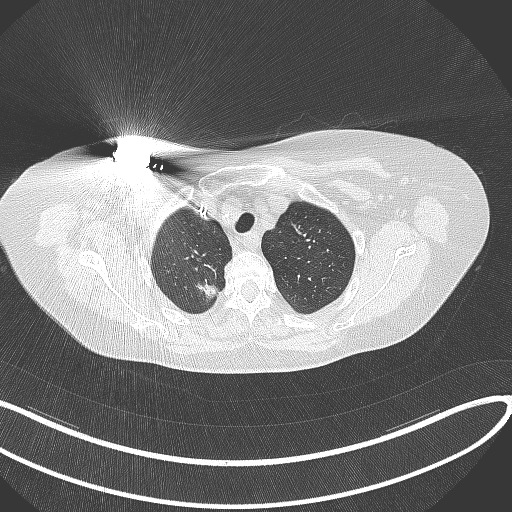
Chest CT, one axial slice; slice 281 of 316 in the series (ordered by position); reconstruction kernel B70f; lung window (W 1500 / L -600 HU); 1 mm slice thickness; 512 × 512 image matrix, field of view 400 × 400 mm. Female patient, age 72 years. Case-level facts recorded for this patient, not image findings: clinical TNM (as recorded): T1c N0 M0.
Outlined on this slice (bounding box drawn by a radiologist):
- lung tumour (recorded histology: adenocarcinoma): bounding box (x1, y1, x2, y2) in pixels: (190, 275, 222, 300)